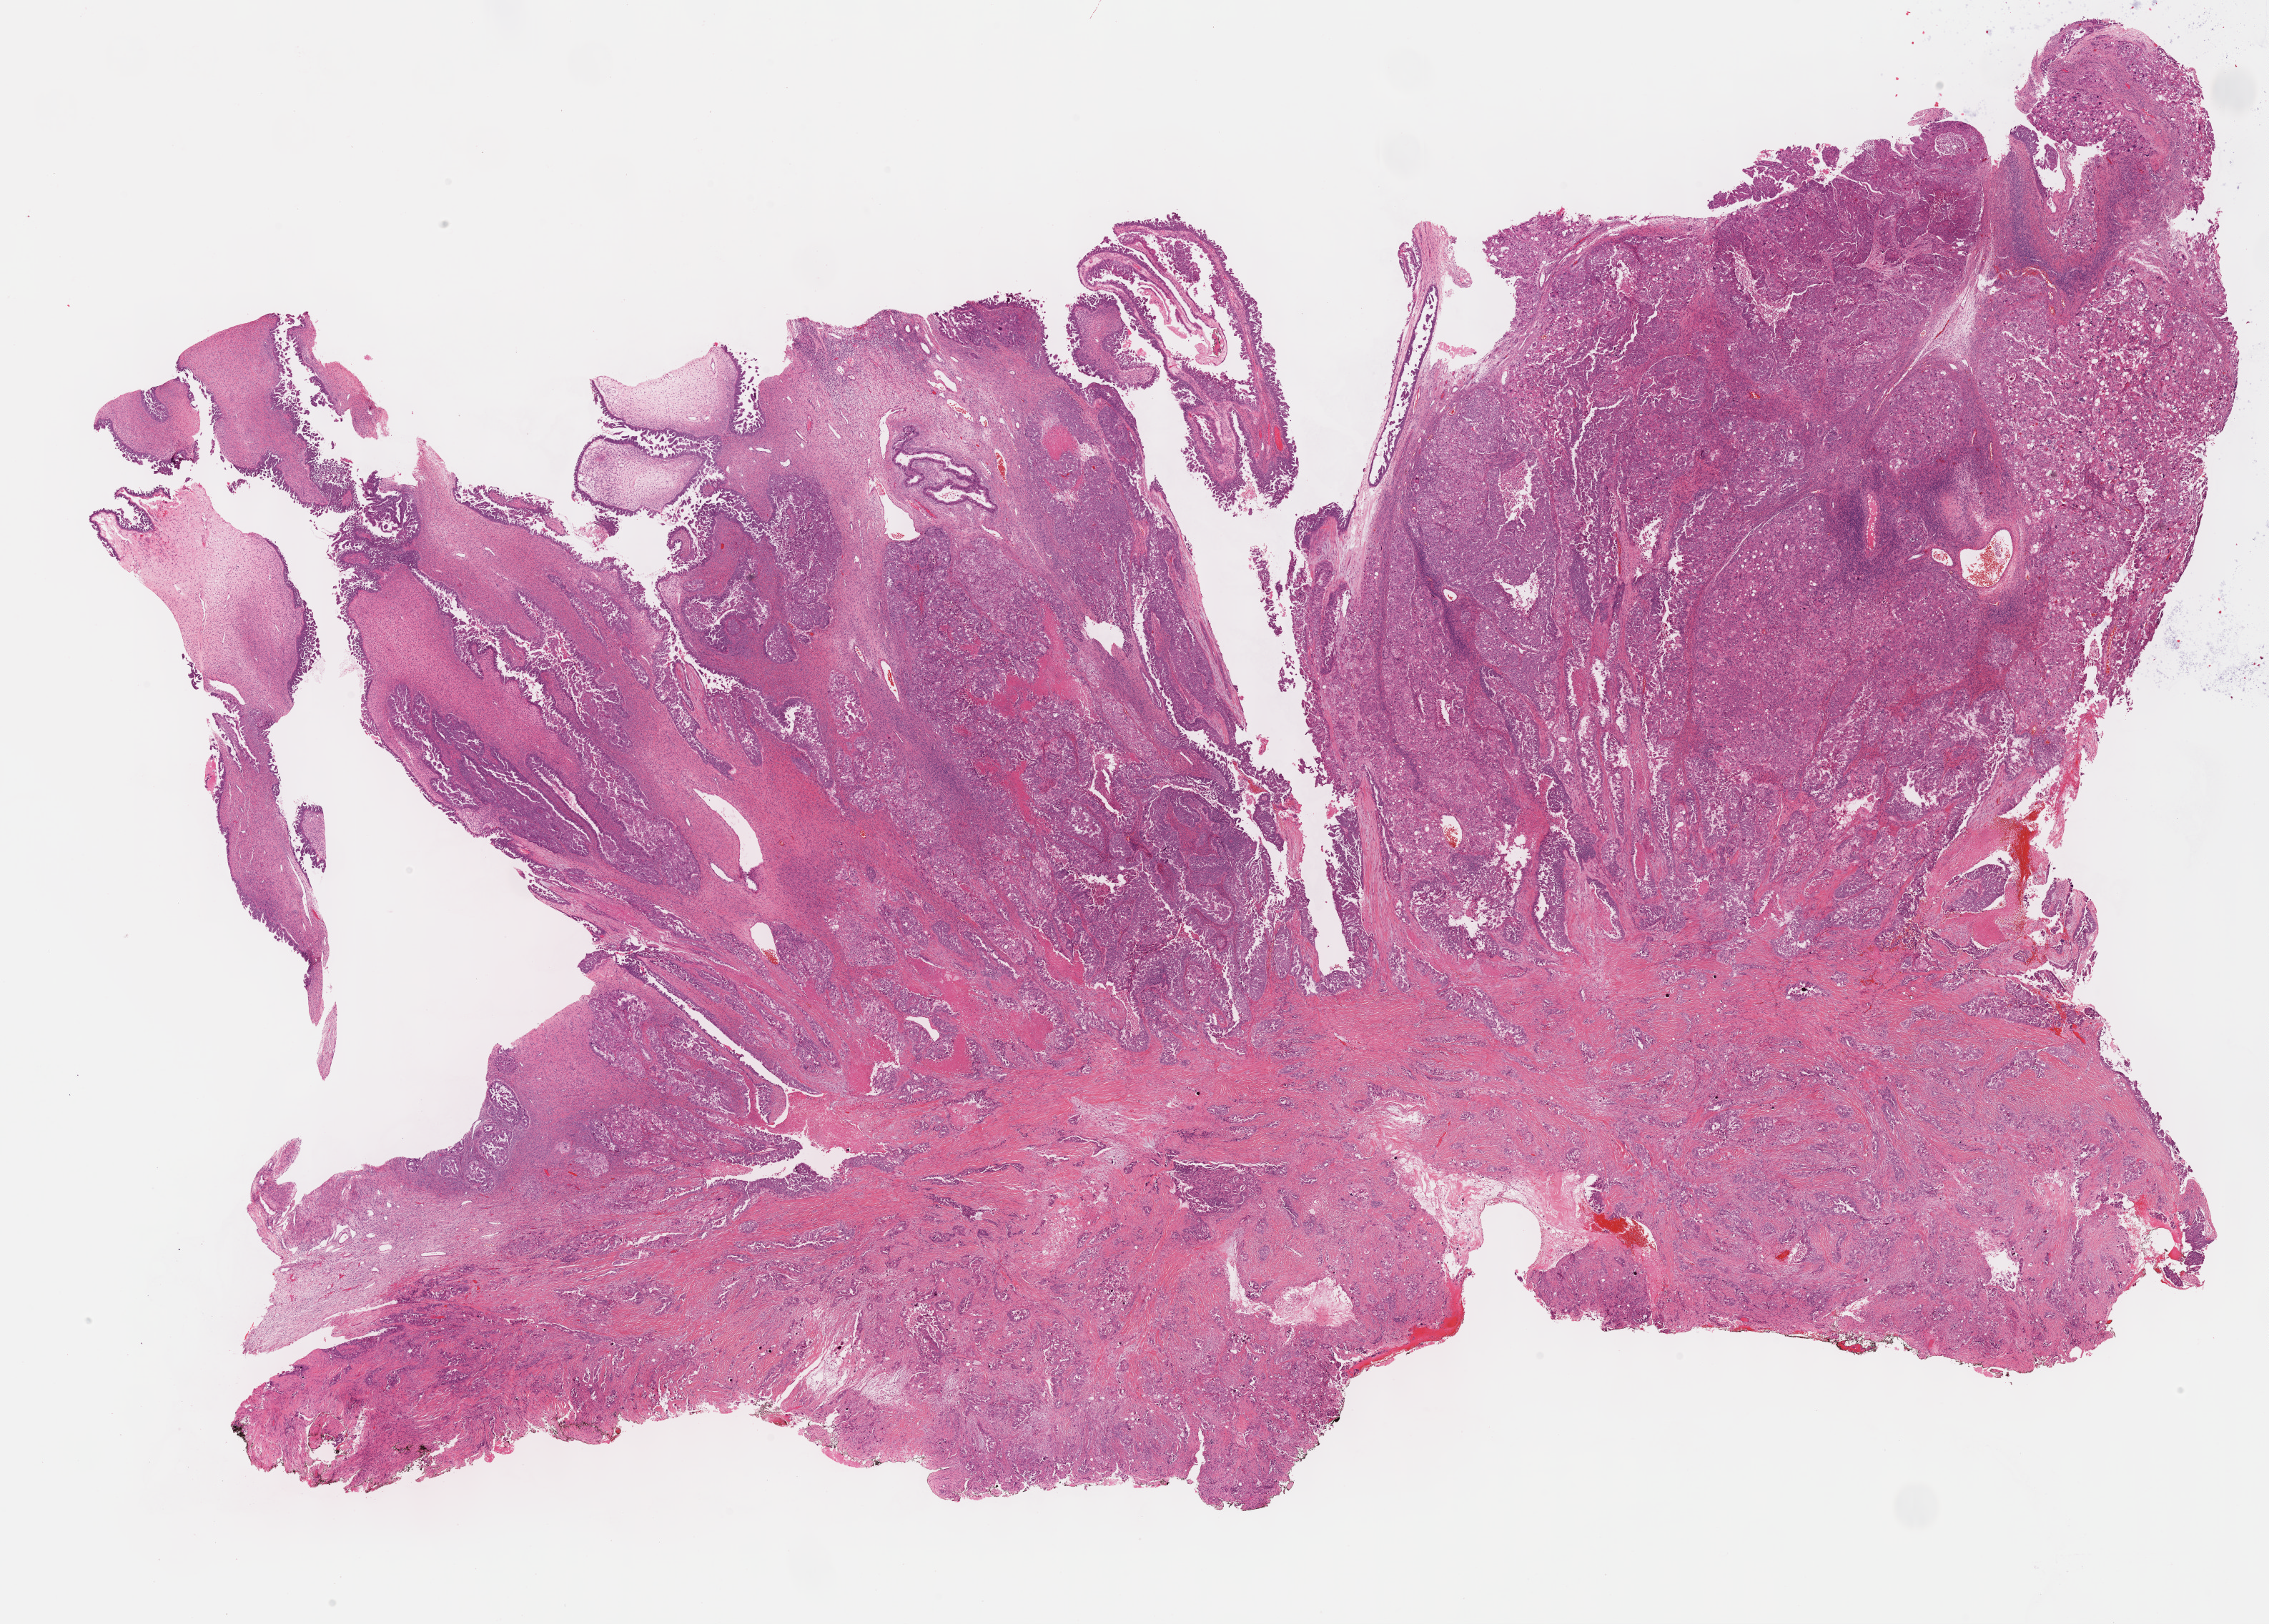
Hematoxylin and eosin (H&E) stained whole-slide image, low-resolution overview of the scanned area, about 25.7 x 18.4 mm, formalin-fixed paraffin-embedded (FFPE) diagnostic section, ovary, primary tumour sample. Female patient; age at initial diagnosis 46 years. Histologic grade: G3 (poorly differentiated).
- histologic diagnosis: Serous cystadenocarcinoma, NOS
- FIGO stage: IIIC
- laterality: right